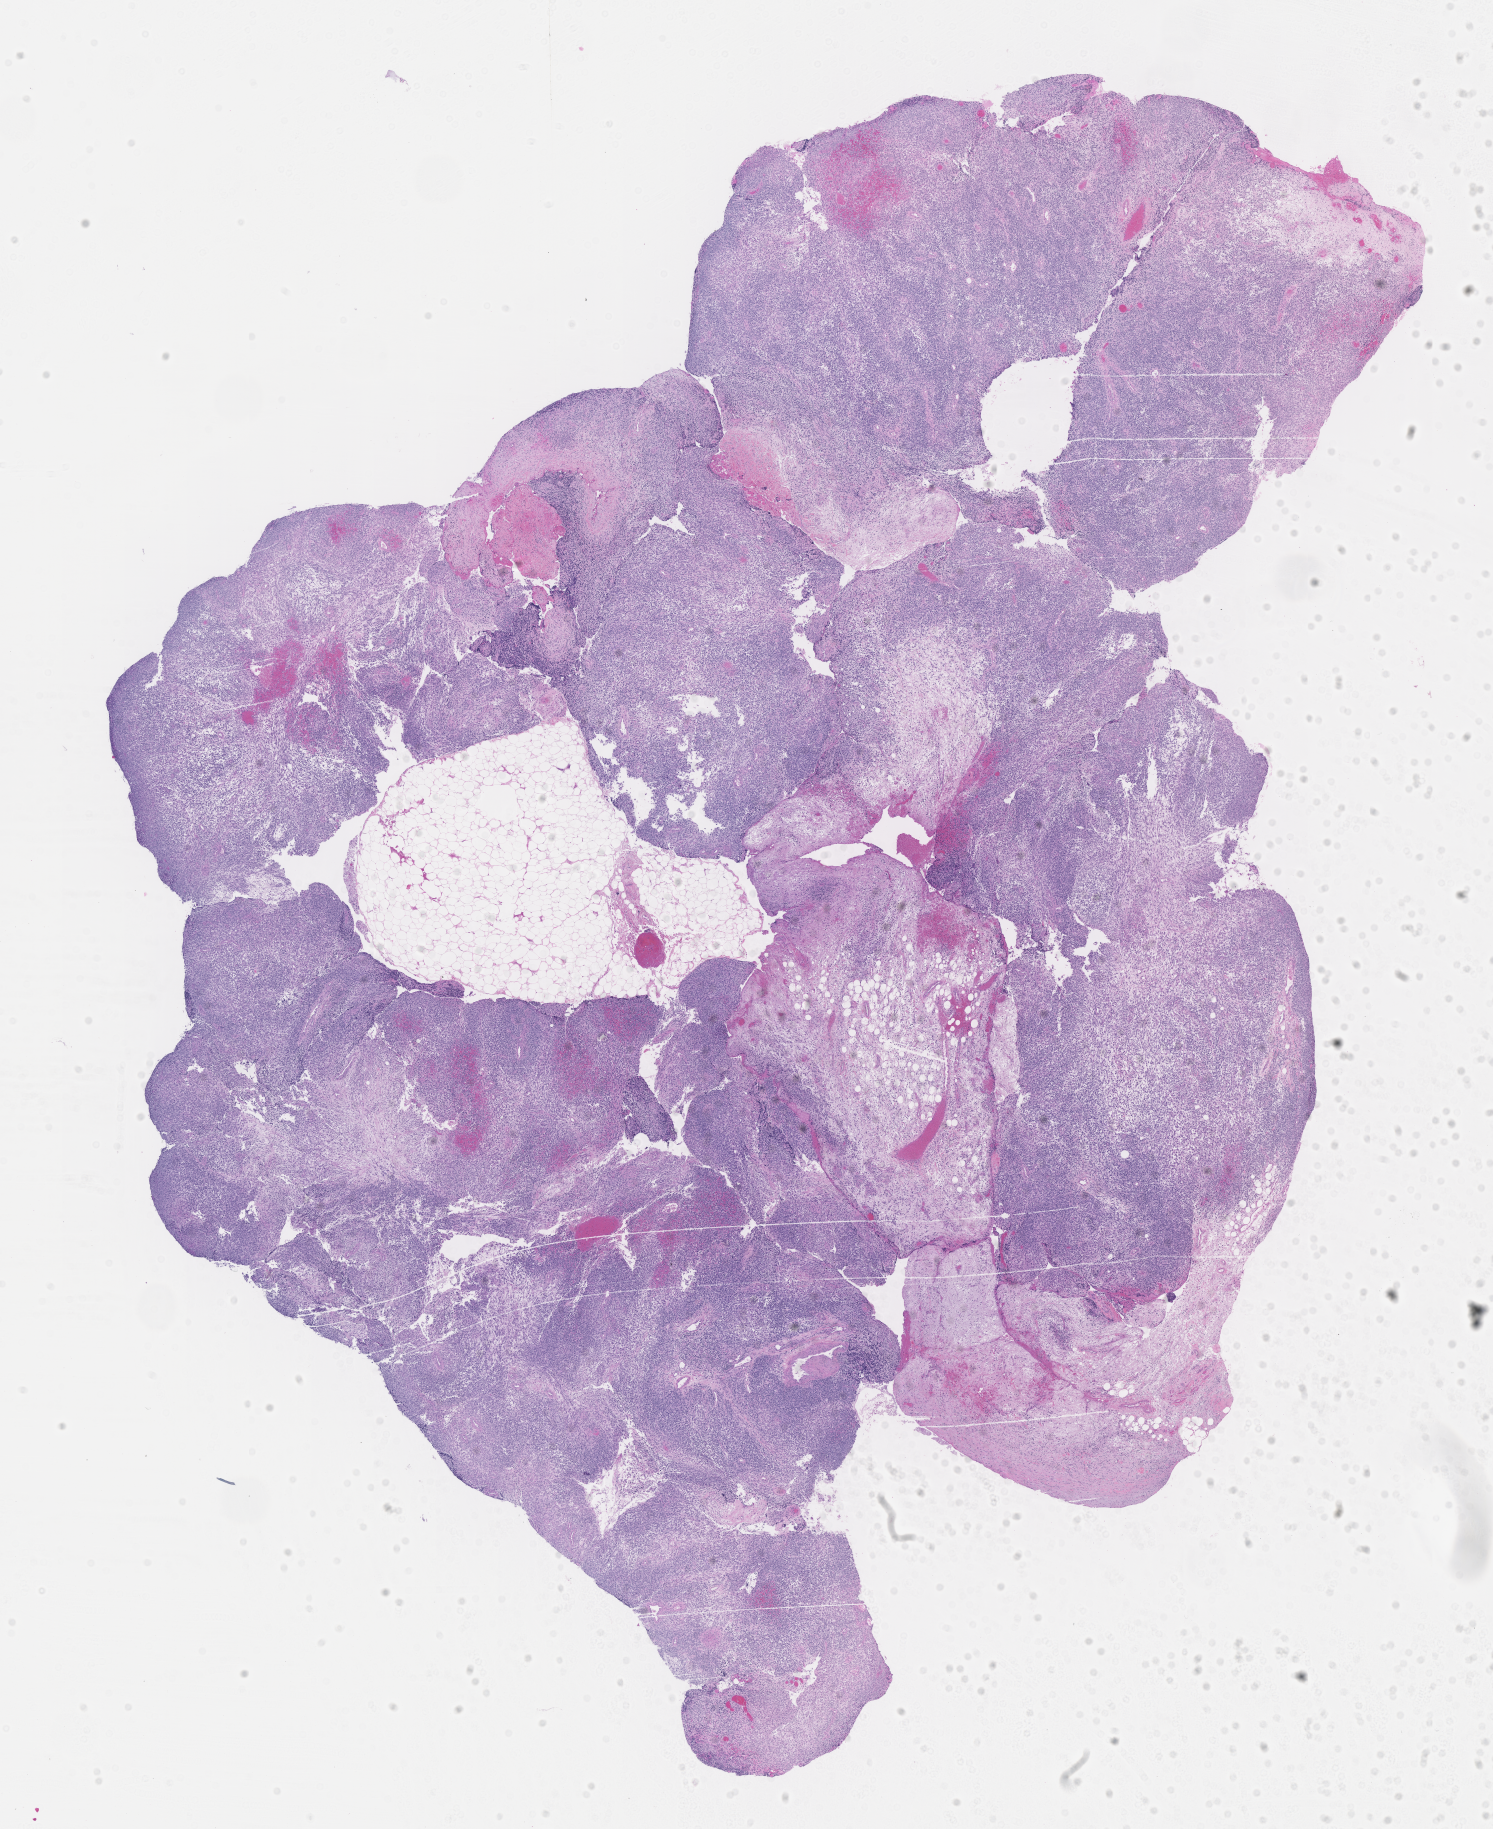
Whole-slide image, haematoxylin and eosin stain of tumor tissue — low-resolution overview of the scanned area, about 12.1 x 14.8 mm. Formalin-fixed, paraffin-embedded (FFPE) tissue. Sample anatomic site: eye, orbit. Patient: male, age 9.8 years at diagnosis.
Diagnosis: rhabdomyosarcoma; histological classification: embryonal rhabdomyosarcoma.